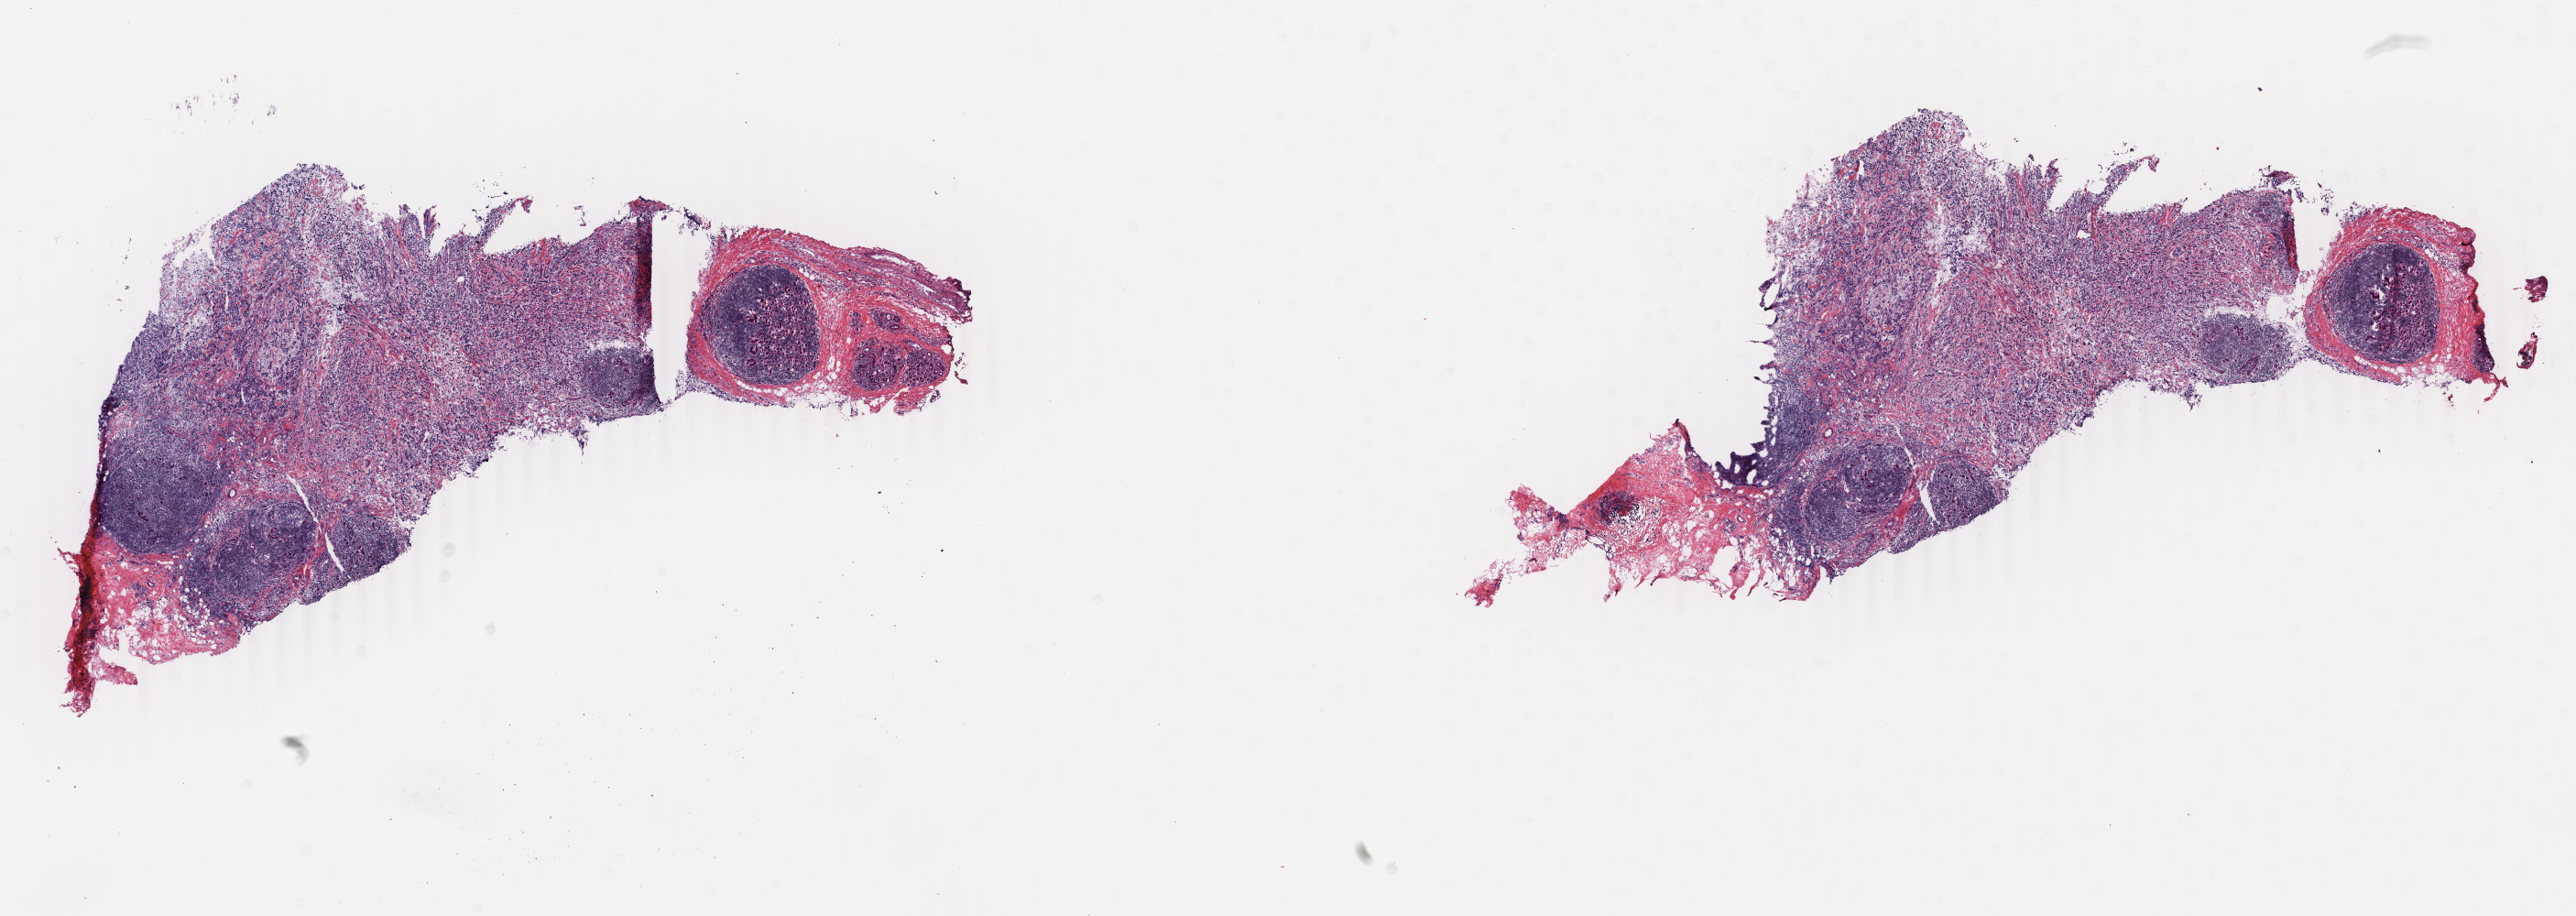
Digitized H&E tissue section (whole slide) — low-resolution overview of the scanned area, about 22.4 x 8.0 mm (slide scanned at 40x), frozen section from the bottom of the tissue portion, breast, primary tumour sample. Female, age 41 years at initial diagnosis. Slide review estimates, as recorded: tumour cells 60%, tumour nuclei 60%.
Diagnosis: Infiltrating duct carcinoma, NOS.